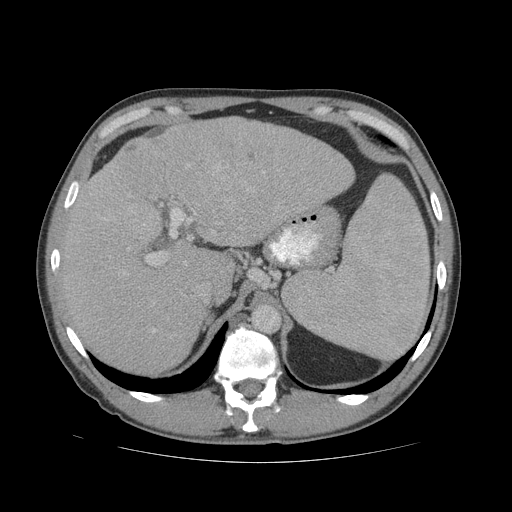
Contrast-enhanced abdominal CT (liver protocol), one axial slice. Position 48 of 81 along the scan axis. 140 kVp. Soft-tissue window (W 400 / L 40 HU). 2.5 mm slice thickness. 512 × 512 image matrix, field of view 400 × 400 mm. From the clinical record (not read from this slice): diagnosis: hepatocellular carcinoma (patient treated with transarterial chemoembolisation; whether this scan precedes or follows treatment is not stated here); TNM stage (as recorded): Stage-IVB; Child-Pugh class: B; tumour differentiation: well differentiated; tumour nodularity: multinodular.
Outlined on this slice (semi-automatically segmented with operator editing):
- liver parenchyma outside the tumour (the mass and vessels are separate outlines, so this box may not span the whole liver): bounding box <60,116,354,374> (left, top, right, bottom; pixels)
- mass: <115,122,218,205>
- liver vessels: <103,164,265,333>